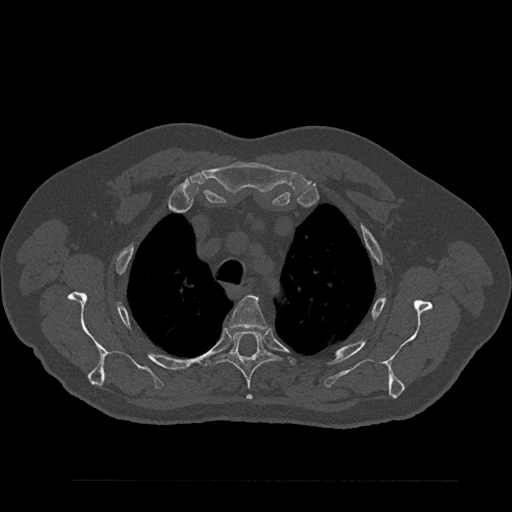
CT including the spine, one axial slice. Position 654 of 797 along the scan axis. Reconstruction kernel Br40s/3. 120 kVp. Bone window (W 1800 / L 400 HU). 0.5 mm slice thickness. 512 × 512 image matrix, field of view 430 × 430 mm. Patient: male, 61 years. From the clinical record (not read from this slice): primary cancer: prostate.
Annotated regions visible in this slice (semi-automatic segmentation, software-assisted and operator-edited):
- T3 vertebra: bounding box (x1, y1, x2, y2) in pixels: (229, 296, 266, 329)
- T4 vertebra: (205, 330, 280, 400)